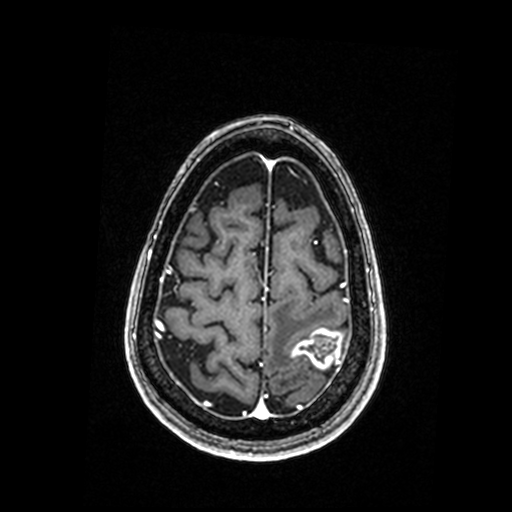
Brain MRI from a brain-tumour surgery series, one axial slice; slice 47 of 192 in the series (ordered by position); T1-weighted post-contrast; 512 × 512 image matrix, field of view 250 × 250 mm. Case-level facts recorded for this patient, not image findings: histopathology: Metastastic Carcinoma, Poorly Differentiated; tumour location: Left Parietal.
Annotated regions visible in this slice (manually delineated by an expert):
- tumour: bounding box (x1, y1, x2, y2) in pixels: (292, 329, 342, 369)